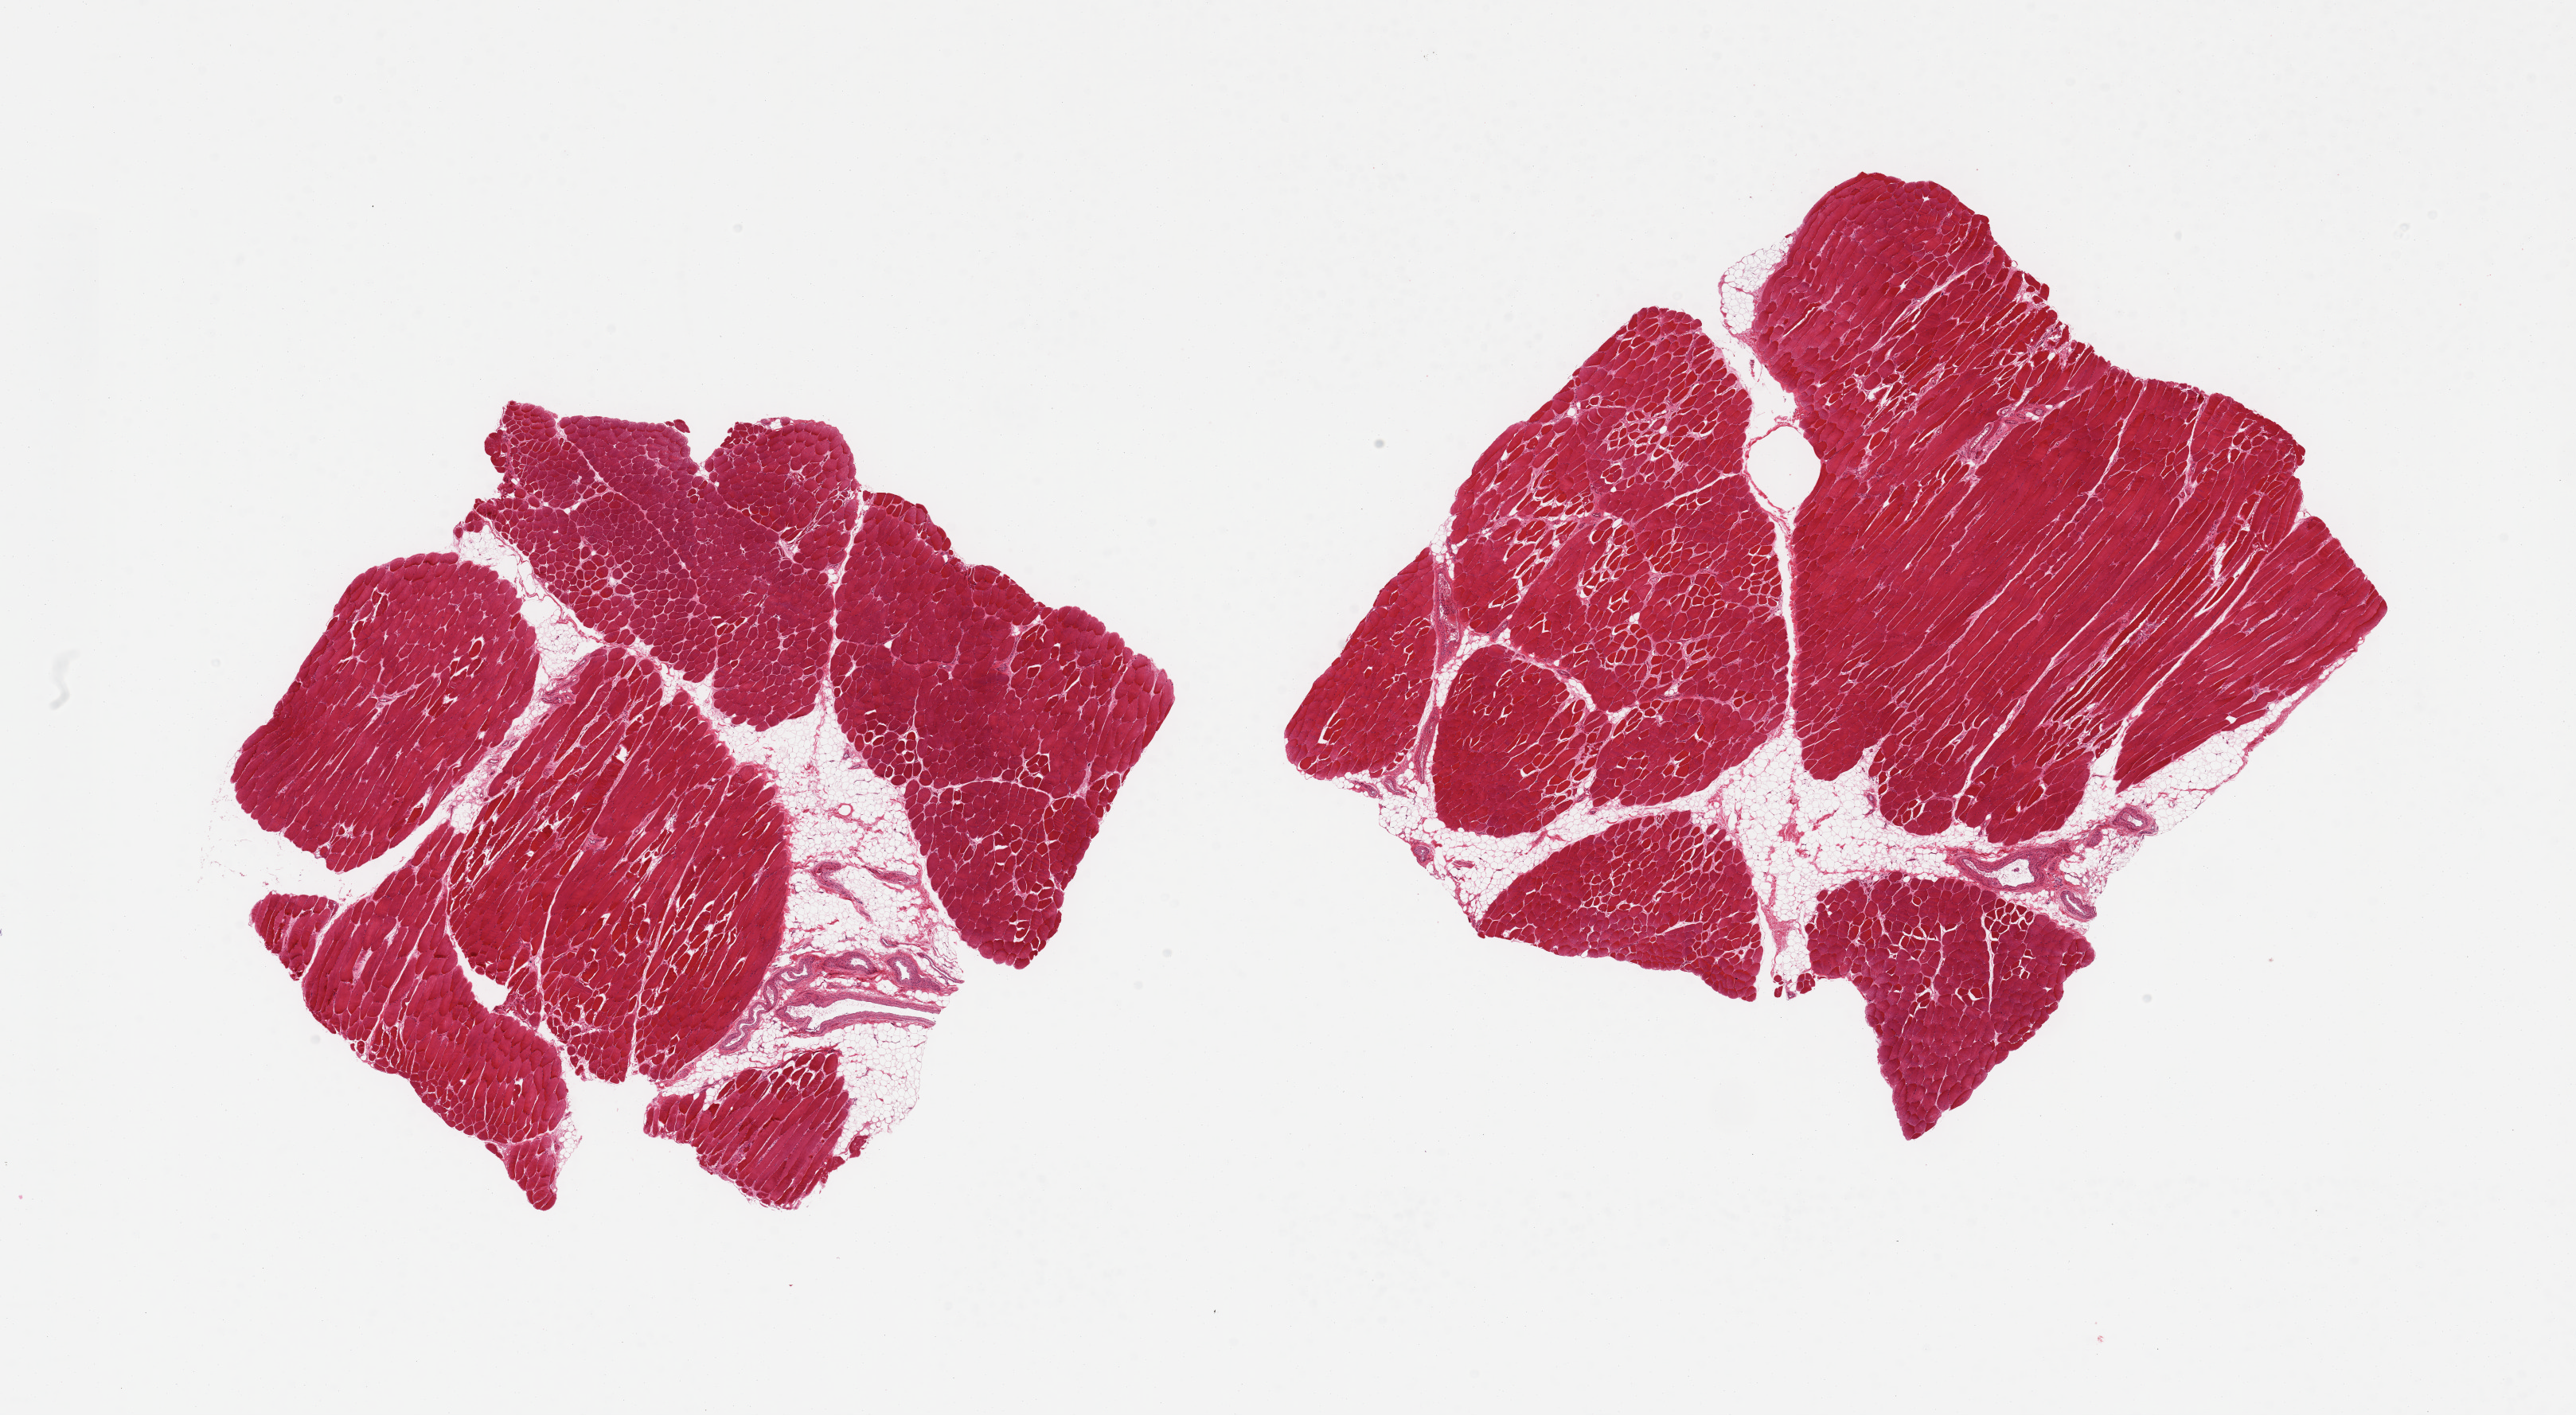
Digitized H&E-stained section, brightfield — whole scanned area (about 25.6 x 14.1 mm) shown as a low-resolution overview. PAXgene-fixed paraffin-embedded (PFPE) section. Target tissue: skeletal muscle. Donor tissue sample. Donor: male.
Pathologist's review note for this sample: 2 pieces; 10 & 20% internal fat.